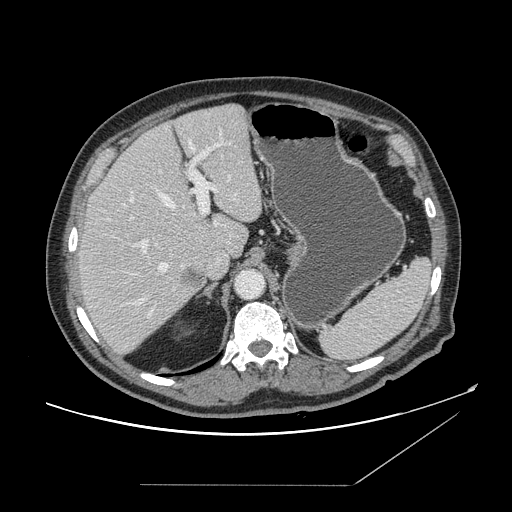
Contrast-enhanced abdominal CT, one axial slice. Position 108 of 166 along the scan axis. Intravenous contrast given. Soft-tissue window (W 400 / L 40 HU). 2.5 mm slice thickness. 512 × 512 image matrix, field of view 416 × 416 mm. Male patient, age 80 years. From the clinical record (not read from this slice): diagnosis: colorectal cancer liver metastases, imaged before liver resection; multiple liver metastases: no; largest metastasis: 2.2 cm; disease in both lobes: no.
Annotated regions visible in this slice (manually delineated by an expert):
- hepatic veins: bounding box <131,140,195,306> (left, top, right, bottom; pixels)
- liver: <79,105,262,355>
- planned liver remnant (the part of the liver to remain after resection): <86,105,262,258>
- portal vein (with intrahepatic branches): <131,134,226,316>
- liver metastasis: <186,270,204,290>
- liver metastasis: <180,268,206,287>